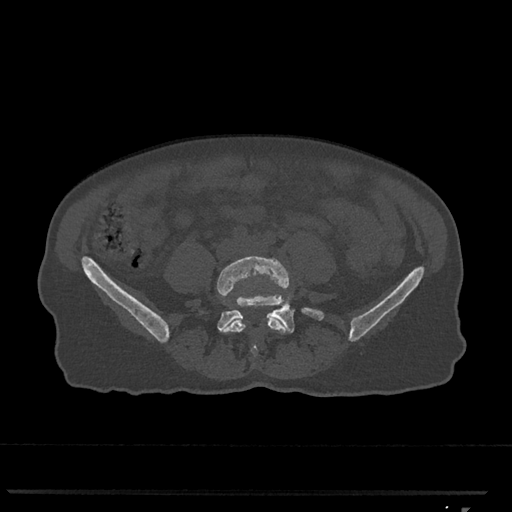
CT including the spine, one axial slice; slice 178 of 793 in the series (ordered by position); 120 kVp; bone window (W 1800 / L 400 HU); 0.5 mm slice thickness; 512 × 512 image matrix, field of view 380 × 380 mm. Patient: female, 62 years. Case-level facts recorded for this patient, not image findings: primary cancer: renal.
Annotated regions visible in this slice (semi-automatic segmentation, software-assisted and operator-edited):
- L4 vertebra: bounding box [x1, y1, x2, y2] px = [217, 256, 289, 356]
- L5 vertebra: [217, 284, 324, 333]